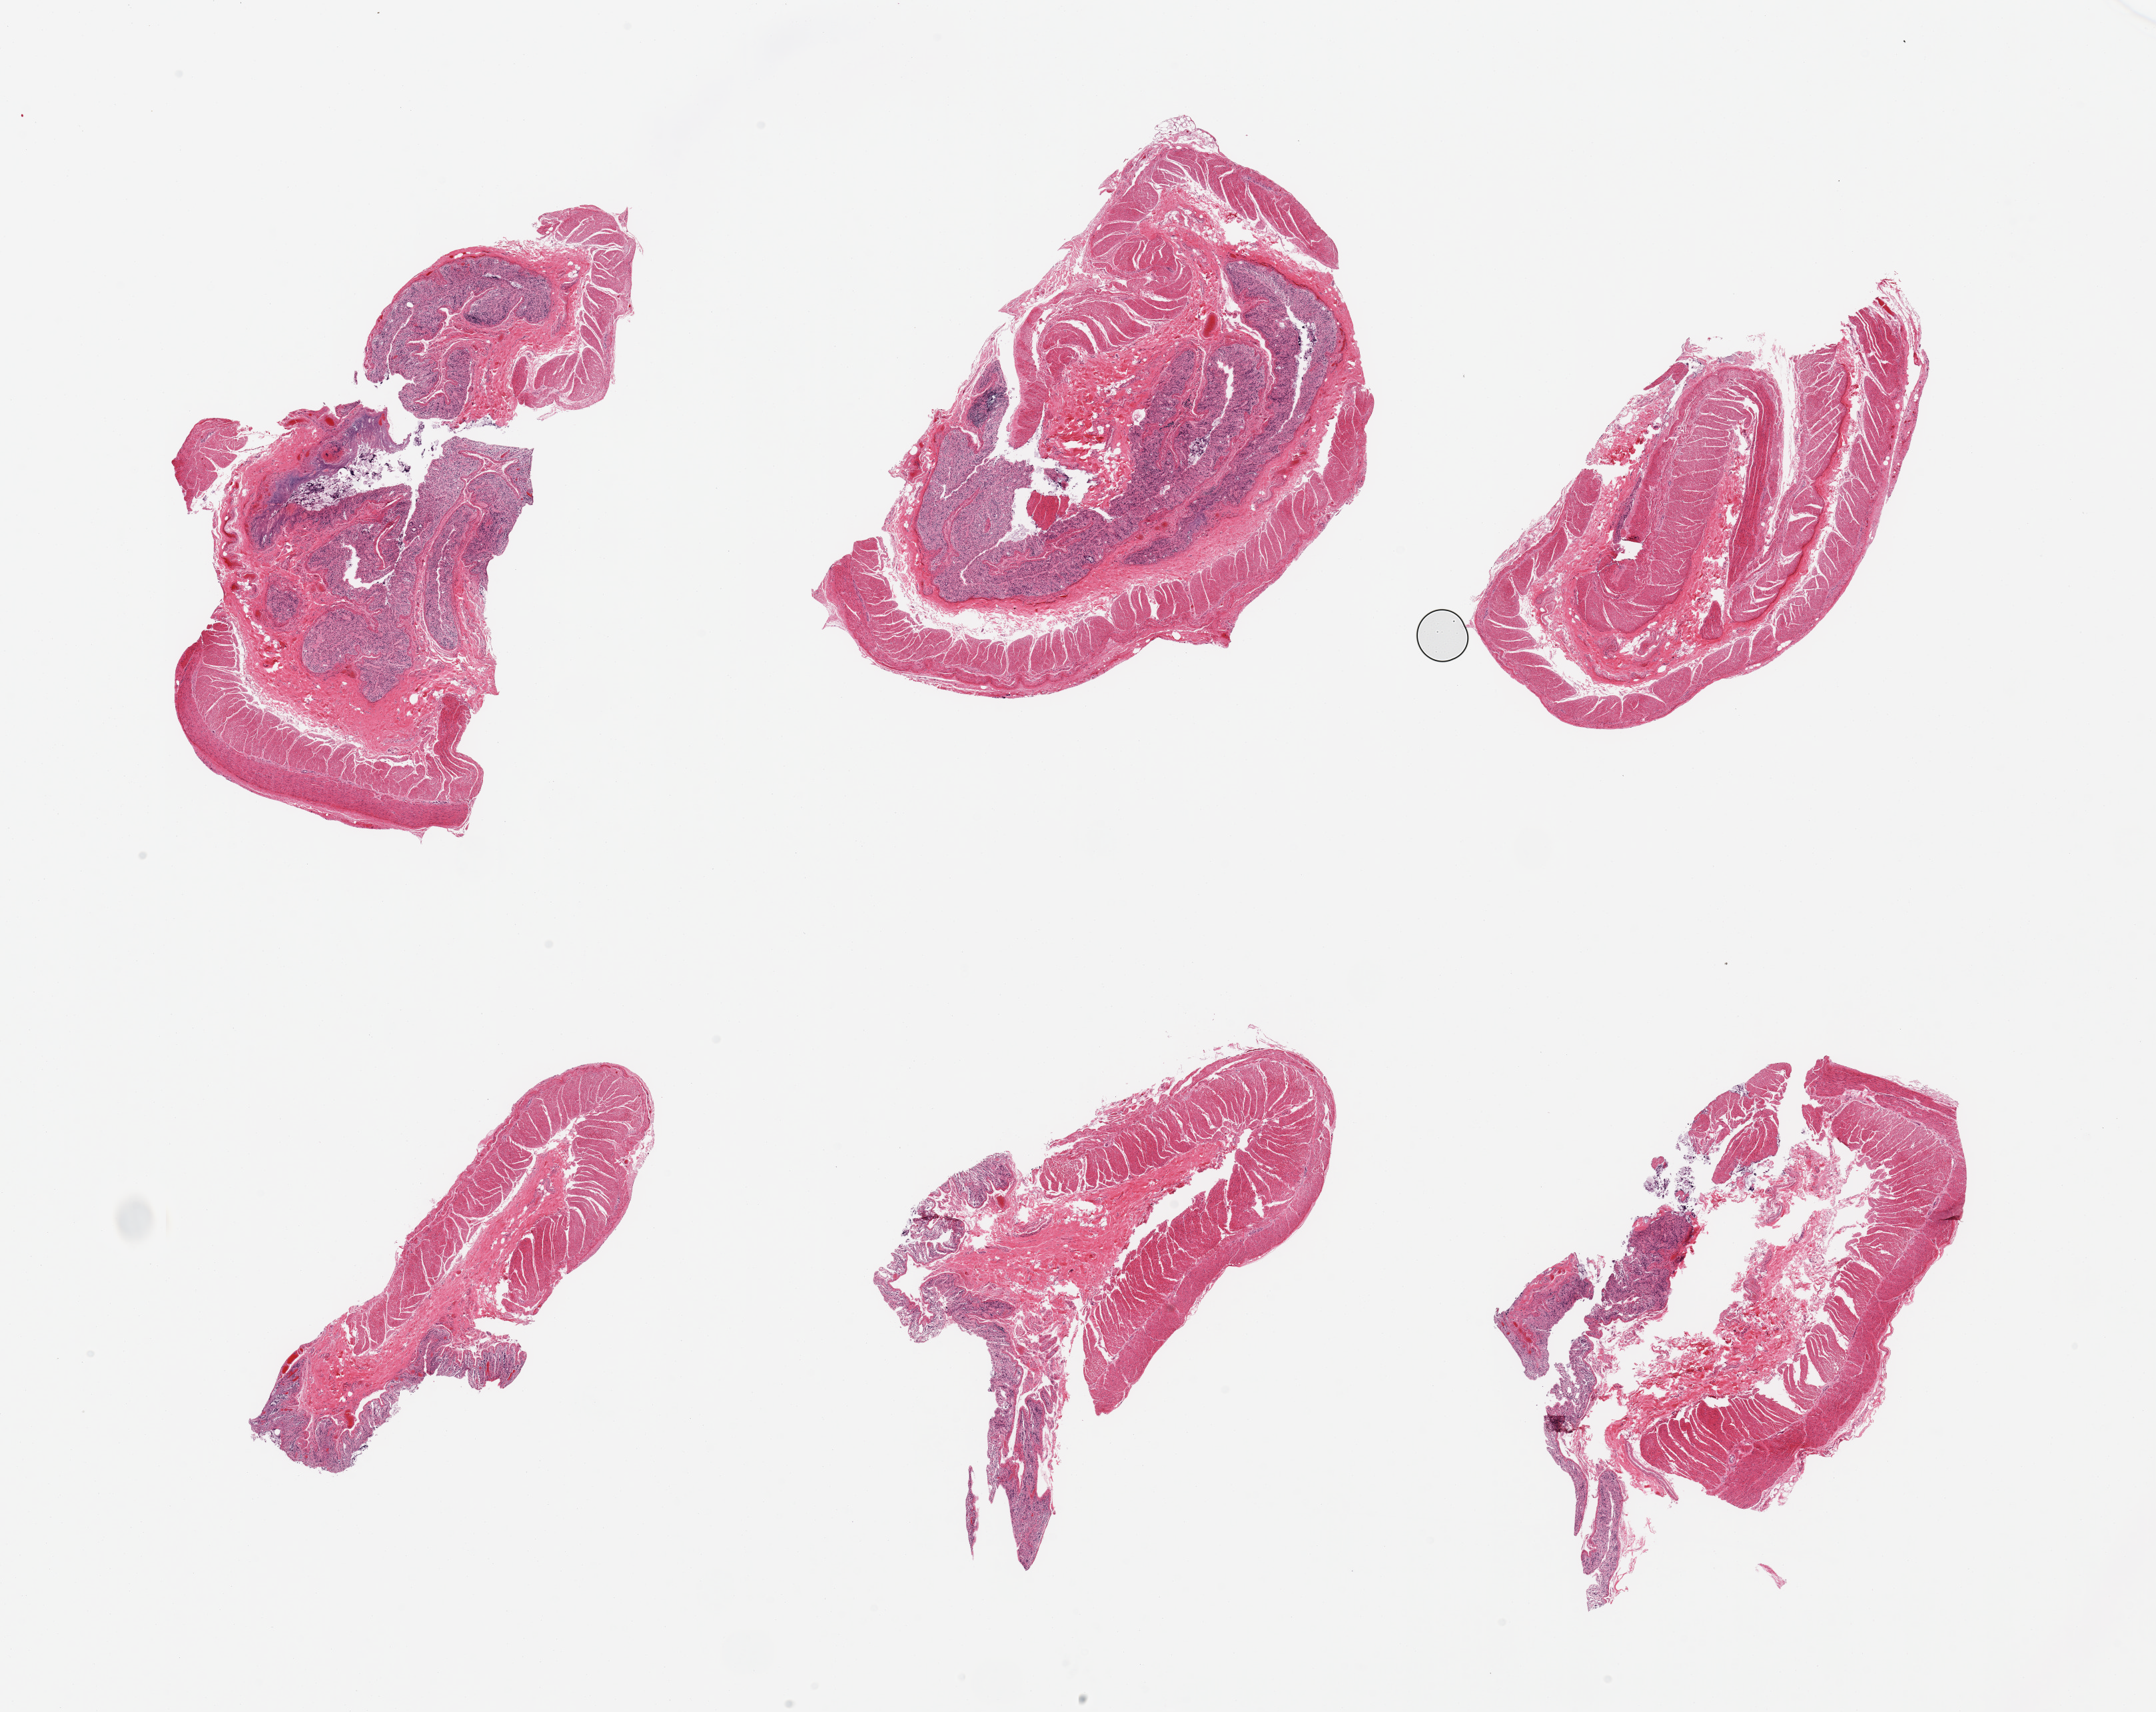
Whole-slide image, haematoxylin and eosin stain — shown as a low-resolution overview of the whole scanned area (about 25.6 x 20.3 mm, from a 20x scan); PAXgene-fixed, paraffin-embedded tissue; sampled site (target tissue): transverse colon; donor tissue sample.
Reviewer comment on this tissue sample: 6 pieces; mucosa autolyzed, muscle intact.